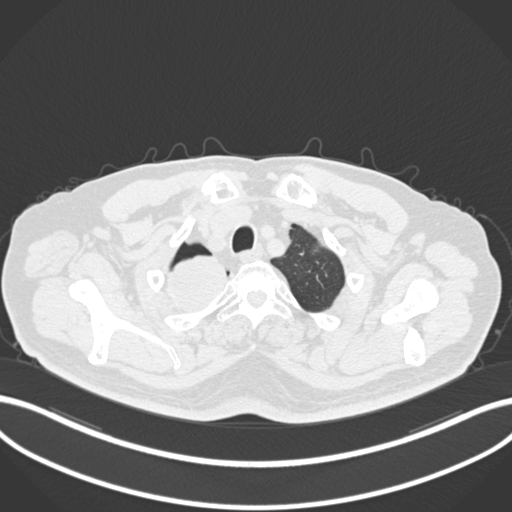
Chest CT, one axial slice; slice 193 of 218 in the series (ordered by position); 120 kVp; lung window (W 1500 / L -600 HU); 1 mm slice thickness; 512 × 512 image matrix, field of view 400 × 400 mm. Patient: male, 68 years. From the clinical record (not read from this slice): clinical TNM (as recorded): T2a N0 M0.
Structures marked on this image (bounding box drawn by a radiologist):
- lung tumour (recorded histology: adenocarcinoma): box from (x=159, y=244) to (x=238, y=317) px